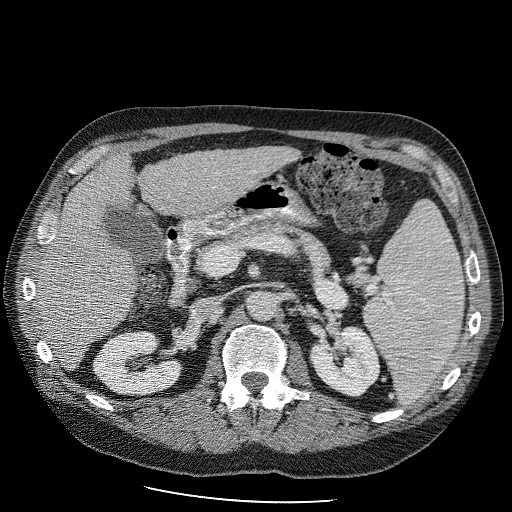
Contrast-enhanced abdominal CT (liver protocol), one axial slice. Slice 44 of 98 in the series (ordered by position). 120 kVp. Soft-tissue window (W 400 / L 40 HU). 2.5 mm slice thickness. 512 × 512 image matrix, field of view 400 × 400 mm. Case-level facts recorded for this patient, not image findings: diagnosis: hepatocellular carcinoma (patient treated with transarterial chemoembolisation; whether this scan precedes or follows treatment is not stated here); TNM stage (as recorded): Stage-II; Child-Pugh class: B; tumour differentiation: moderately differentiated; tumour nodularity: uninodular.
Outlined on this slice (semi-automatic segmentation, software-assisted and operator-edited):
- liver parenchyma outside the tumour (the mass and vessels are separate outlines, so this box may not span the whole liver): bounding box (x1, y1, x2, y2) in pixels: (34, 146, 298, 368)
- liver vessels: (45, 216, 87, 282)